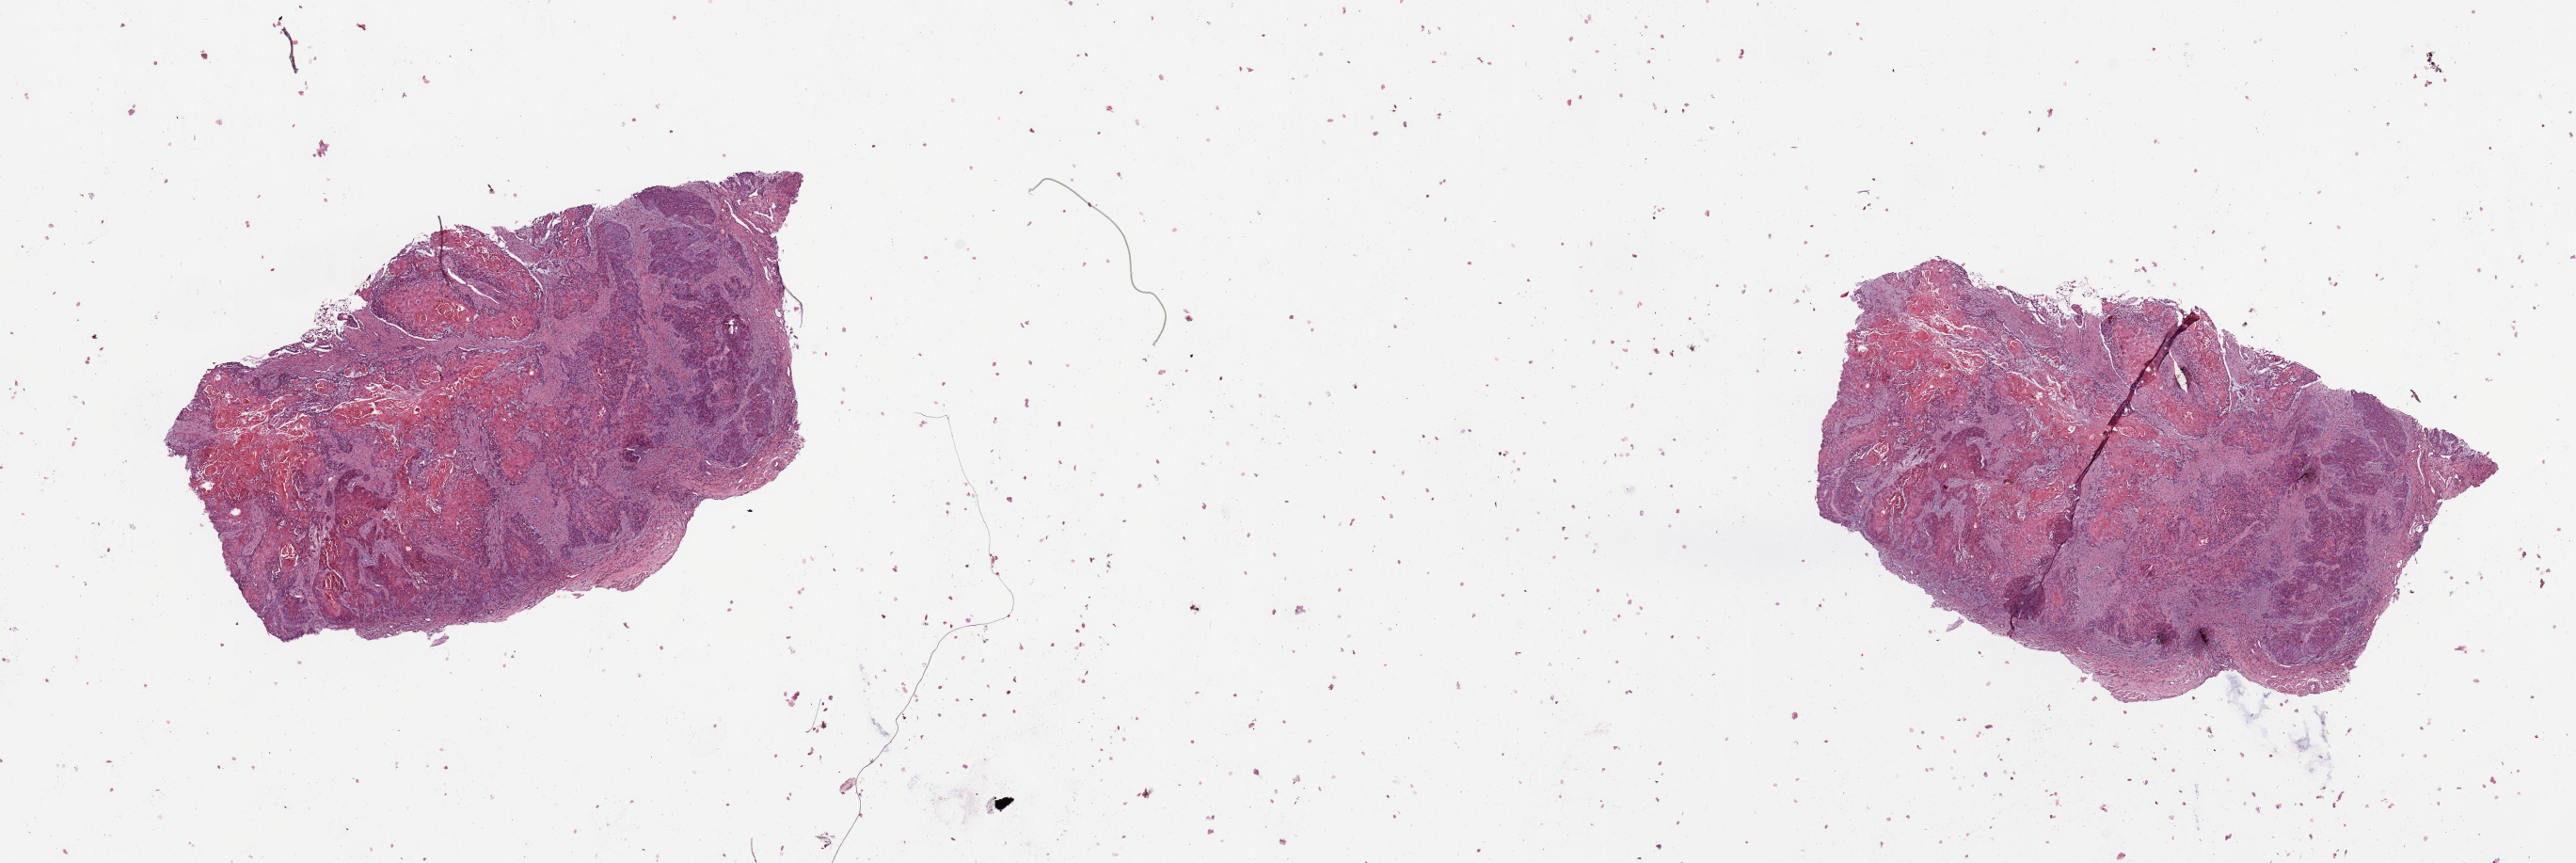
Digitized H&E tissue section (whole slide), a low-resolution overview of the entire scanned area, about 21.7 x 7.3 mm; tumour tissue sample, sampled site: larynx. 50-year-old male patient. Histologic grade: G2 (moderately differentiated). Slide review estimates, as recorded: tumour nuclei 80%, necrosis 5%.
- primary tumour site (as recorded): larynx
- diagnosis: Squamous cell carcinoma, NOS
- AJCC pathologic stage: III